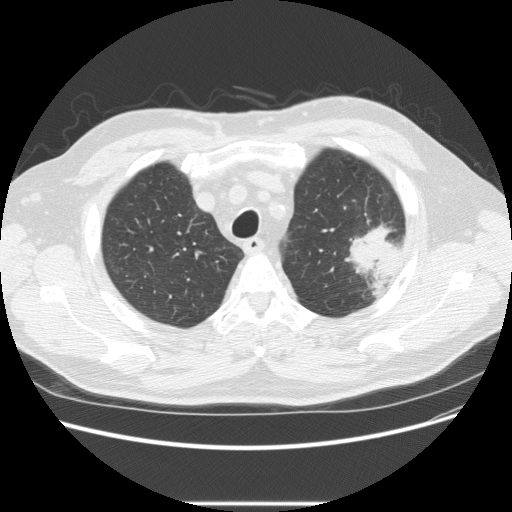
Axial slice from a low-dose chest CT screening exam, first (baseline) screen, lung window (W 1500 / L -600 HU), 2.5 mm slice thickness, standard (soft-tissue) reconstruction kernel (STANDARD), 512 × 512 image matrix. Male participant, aged 73 years at enrolment.
Expert-annotated lung lesion, bounding box (x1, y1, x2, y2) in pixels: (332, 216, 411, 284). The screening reader recorded 2 non-calcified nodules or masses ≥4 mm on this exam; which of them this box marks is not recorded. Participant outcome: lung cancer diagnosed 11 days after this screen — bronchiolo-alveolar adenocarcinoma, NOS, other location, well differentiated (G1), stage IV (AJCC 6th edition).